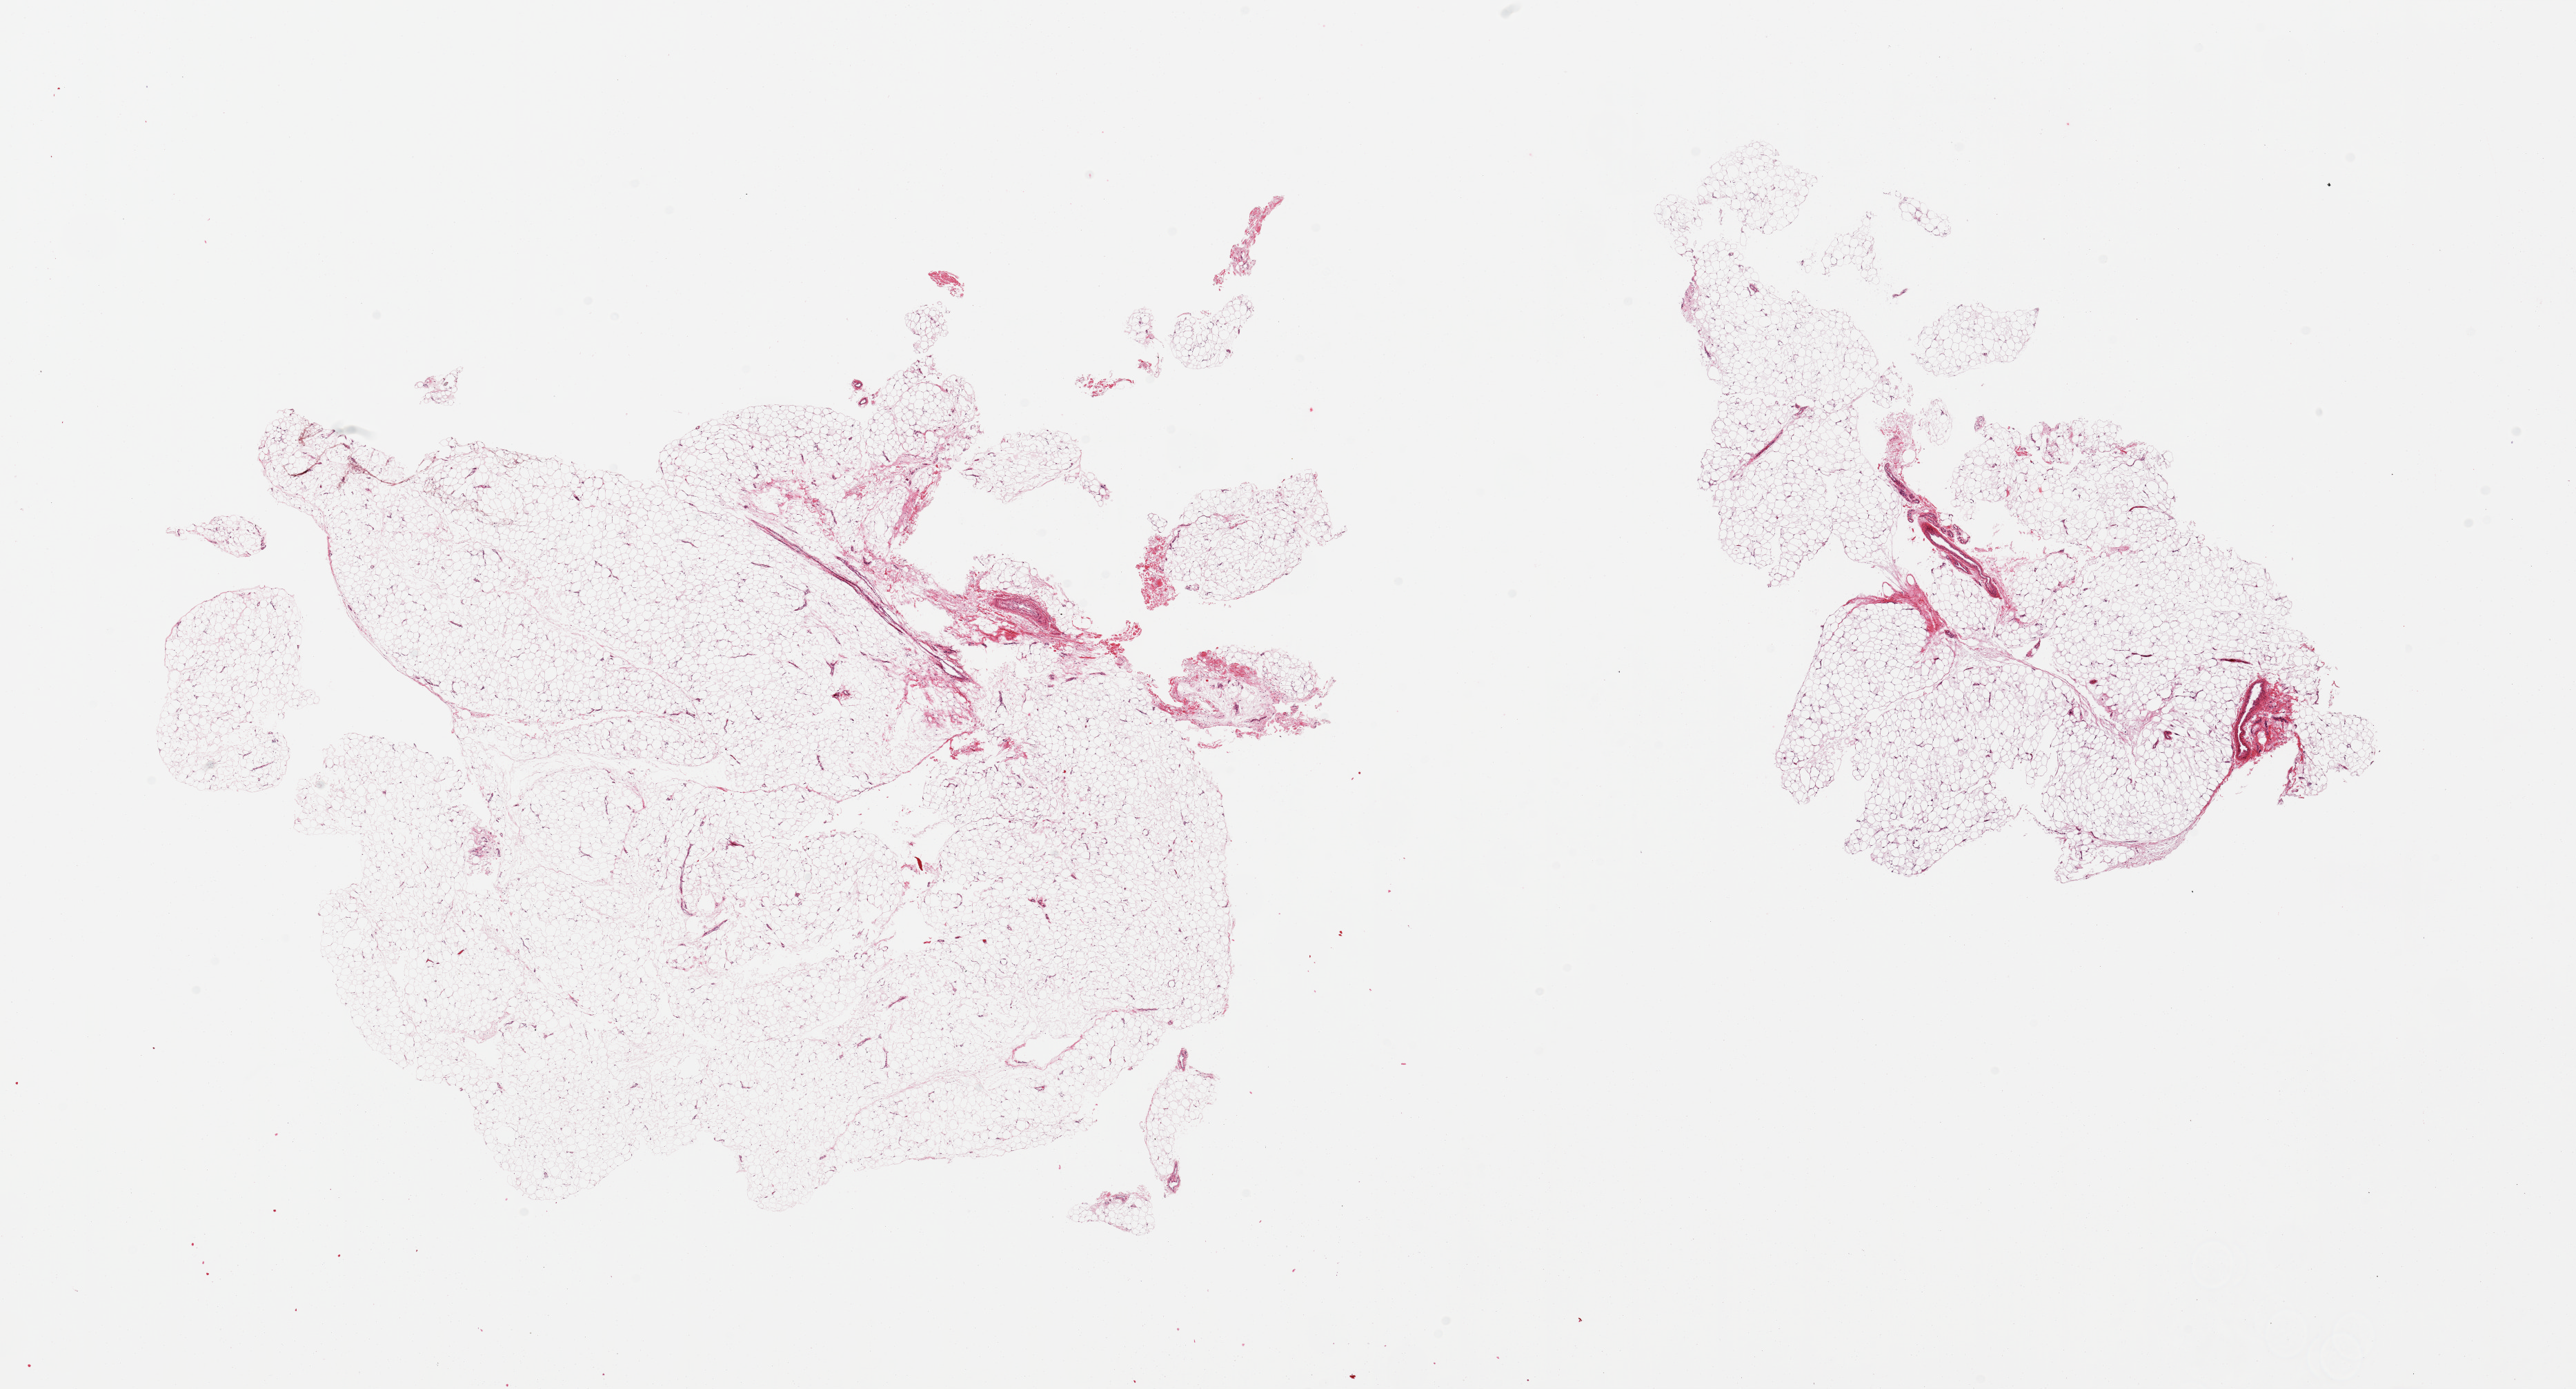
Whole-slide image, hematoxylin and eosin (H&E) stain — a low-resolution overview of the entire scanned area, about 29.5 x 15.9 mm; PAXgene-fixed paraffin-embedded (PFPE) section; target tissue: omentum; tissue donor sample. Female donor.
Pathologist's review note for this sample: 2 pieces.